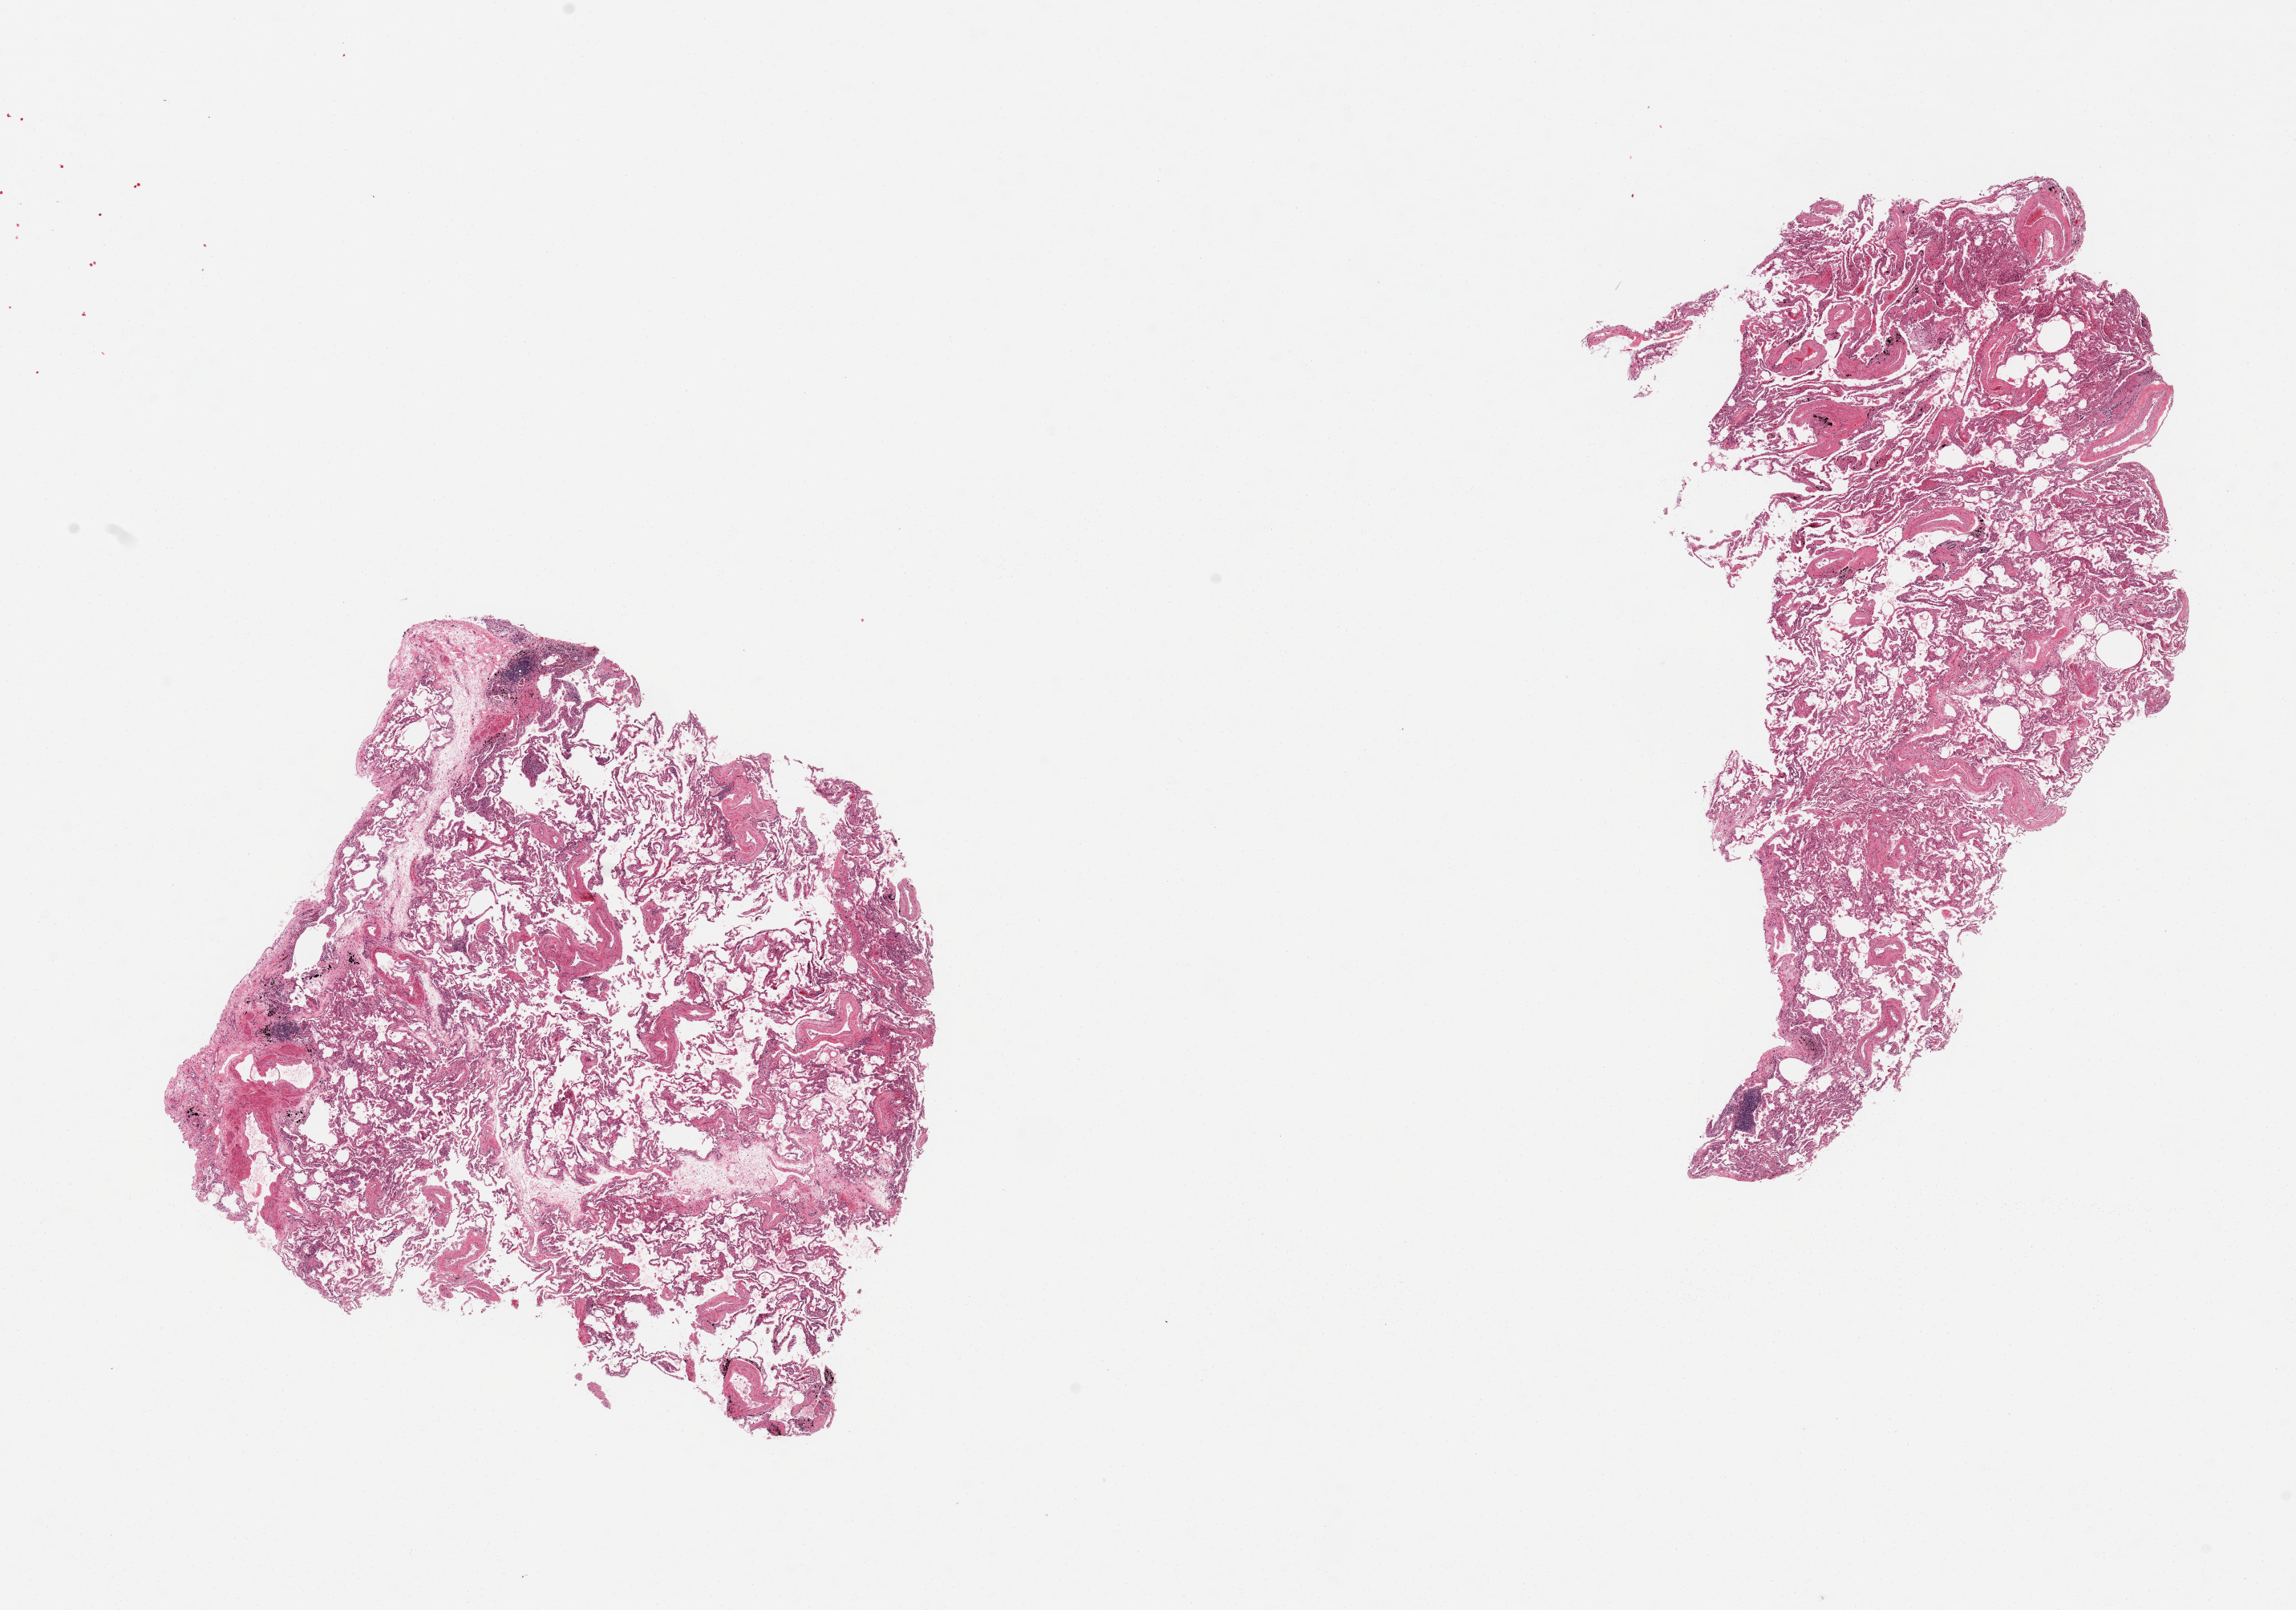
Haematoxylin and eosin whole-slide image, brightfield, low-resolution overview of the scanned area, about 22.6 x 15.9 mm; PAXgene-fixed paraffin-embedded (PFPE) section; section of lung (target tissue); tissue donor sample. Donor sex: male.
Pathologist's review note for this sample: 2 pieces, mild congestion.